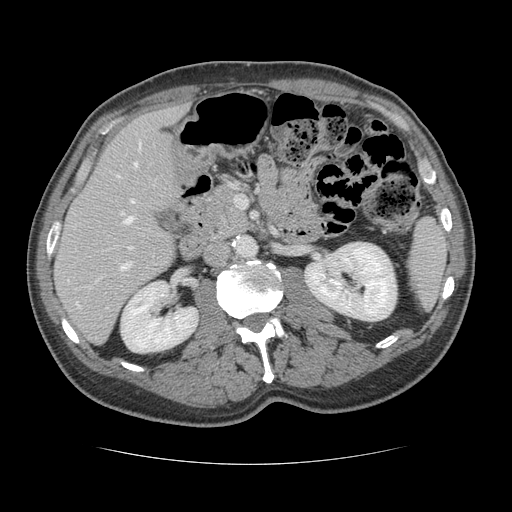
Contrast-enhanced abdominal CT, one axial slice. Position 63 of 134 along the scan axis. Reconstruction kernel STANDARD. 120 kVp. Soft-tissue window (W 400 / L 40 HU). 512 × 512 image matrix, field of view 377 × 377 mm. Male patient, age 68 years. From the clinical record (not read from this slice): diagnosis: colorectal cancer liver metastases, imaged before liver resection; multiple liver metastases: yes; largest metastasis: 2.2 cm.
Annotated regions visible in this slice (manually delineated by an expert):
- hepatic veins: bounding box [x1, y1, x2, y2] px = [76, 142, 141, 306]
- liver: [56, 109, 182, 342]
- planned liver remnant (the part of the liver to remain after resection): [56, 108, 182, 335]
- portal vein (with intrahepatic branches): [121, 212, 133, 270]